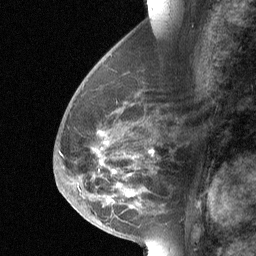
Breast MRI (dynamic contrast-enhanced), one sagittal slice. Slice 28 of 64 in the series (ordered by position). Dynamic contrast-enhanced study with each time point stored as its own series, time point 2 of 3 at this slice position (early post-contrast, ordered by acquisition time). 1.5 T. TE 4.8 ms, TR 27 ms. 256 × 256 image matrix, field of view 180 × 180 mm. Female patient, age 56 years. Case-level facts recorded for this patient, not image findings: setting: breast cancer imaged before/during neoadjuvant chemotherapy; receptor status: HER2-positive.
Outlined on this slice (semi-automatically segmented with operator editing):
- analysis volume of interest (the breast-tissue region the enhancement analysis was run in; not a lesion): bounding box [x1, y1, x2, y2] px = [68, 83, 162, 214]
- tumour enhancement mask (voxels above the 90 % enhancement threshold inside the analysis volume of interest): [106, 142, 131, 193]